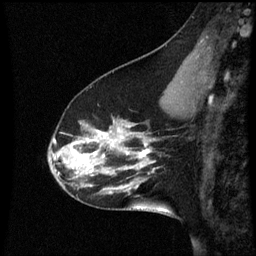
Breast MRI (dynamic contrast-enhanced), one sagittal slice. Position 18 of 60 along the scan axis. Dynamic contrast-enhanced series, image 2 of 3 at this slice position (ordered by acquisition). 1.5 T. TE 4.2 ms, TR 8.9 ms. 2 mm slice thickness. 256 × 256 image matrix, field of view 200 × 200 mm. Patient: female, 45 years. From the clinical record (not read from this slice): setting: breast cancer imaged before/during neoadjuvant chemotherapy; receptor status: HR-positive, HER2-negative.
Outlined on this slice (semi-automatic segmentation, software-assisted and operator-edited):
- analysis volume of interest (the breast-tissue region the enhancement analysis was run in; not a lesion): bounding box [x1, y1, x2, y2] px = [48, 94, 171, 205]
- tumour enhancement mask (voxels above the 70 % enhancement threshold inside the analysis volume of interest): [72, 130, 149, 187]